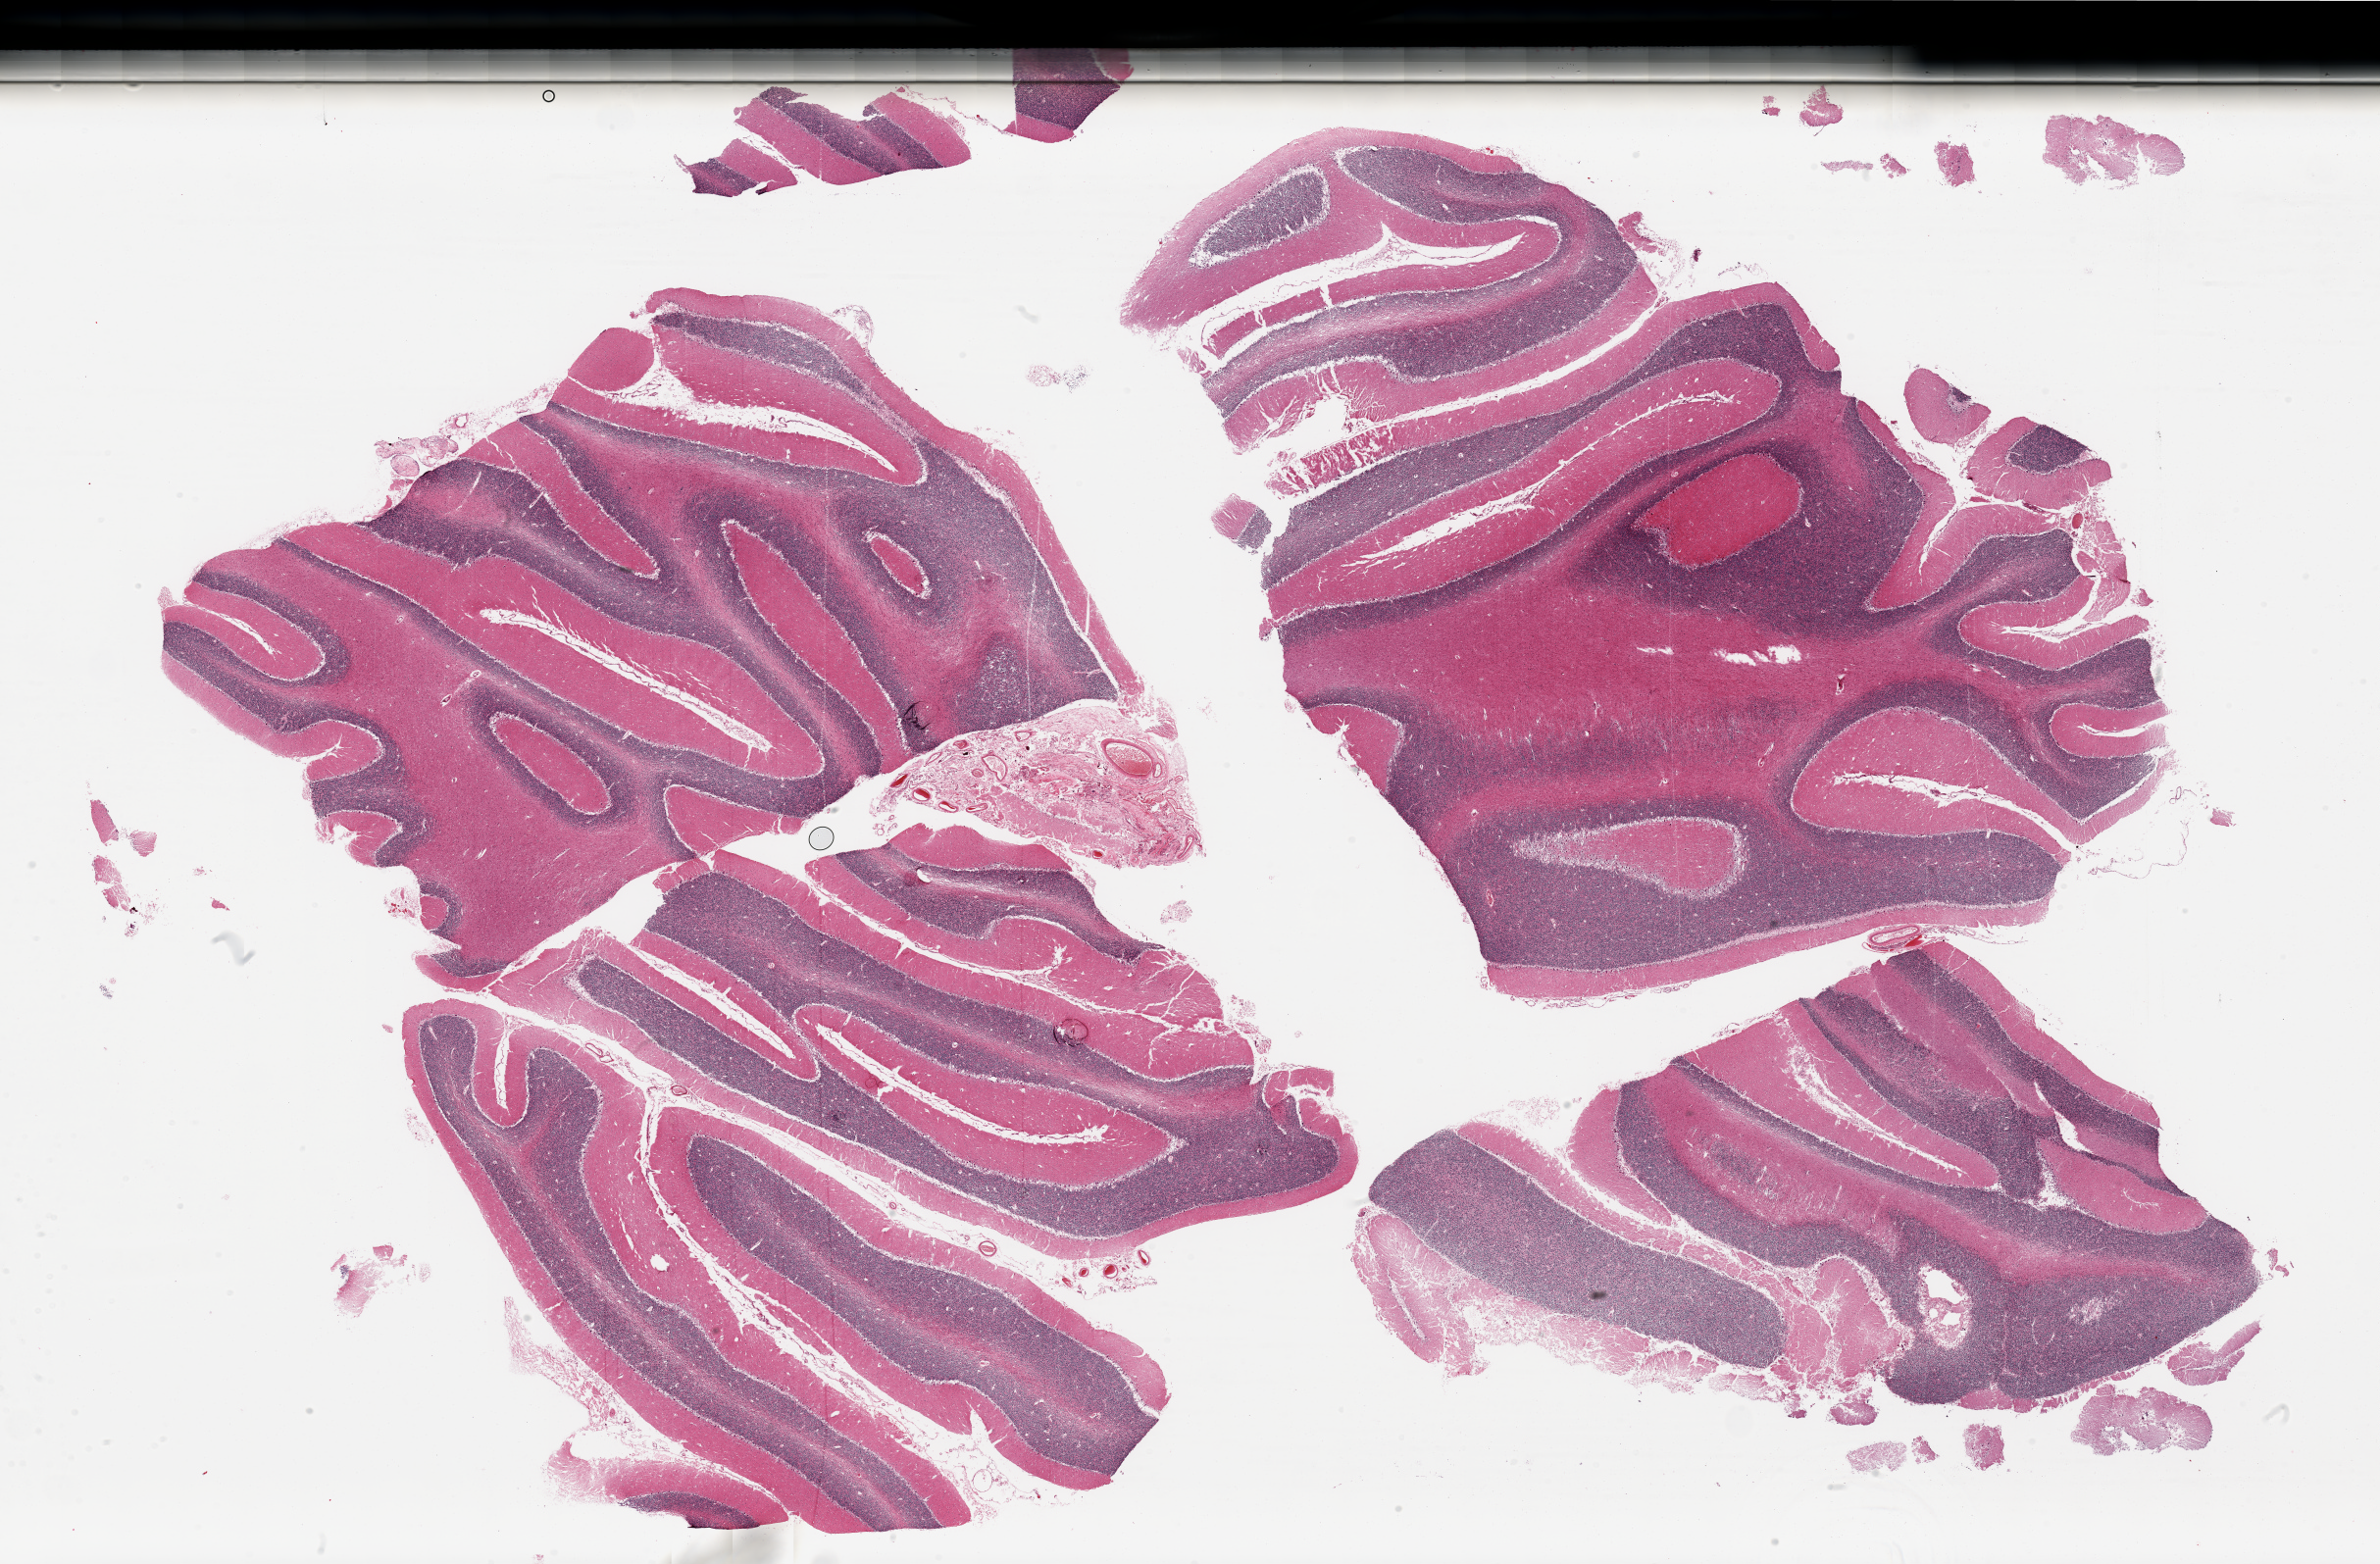
Whole-slide image, H&E stain — shown as a low-resolution overview of the whole scanned area (about 38.4 x 25.2 mm), PAXgene-fixed, paraffin-embedded tissue, section of cerebellum (target tissue), donor tissue sample. Male donor.
* pathologist's review note for this sample: 4 pieces, no abnormalities